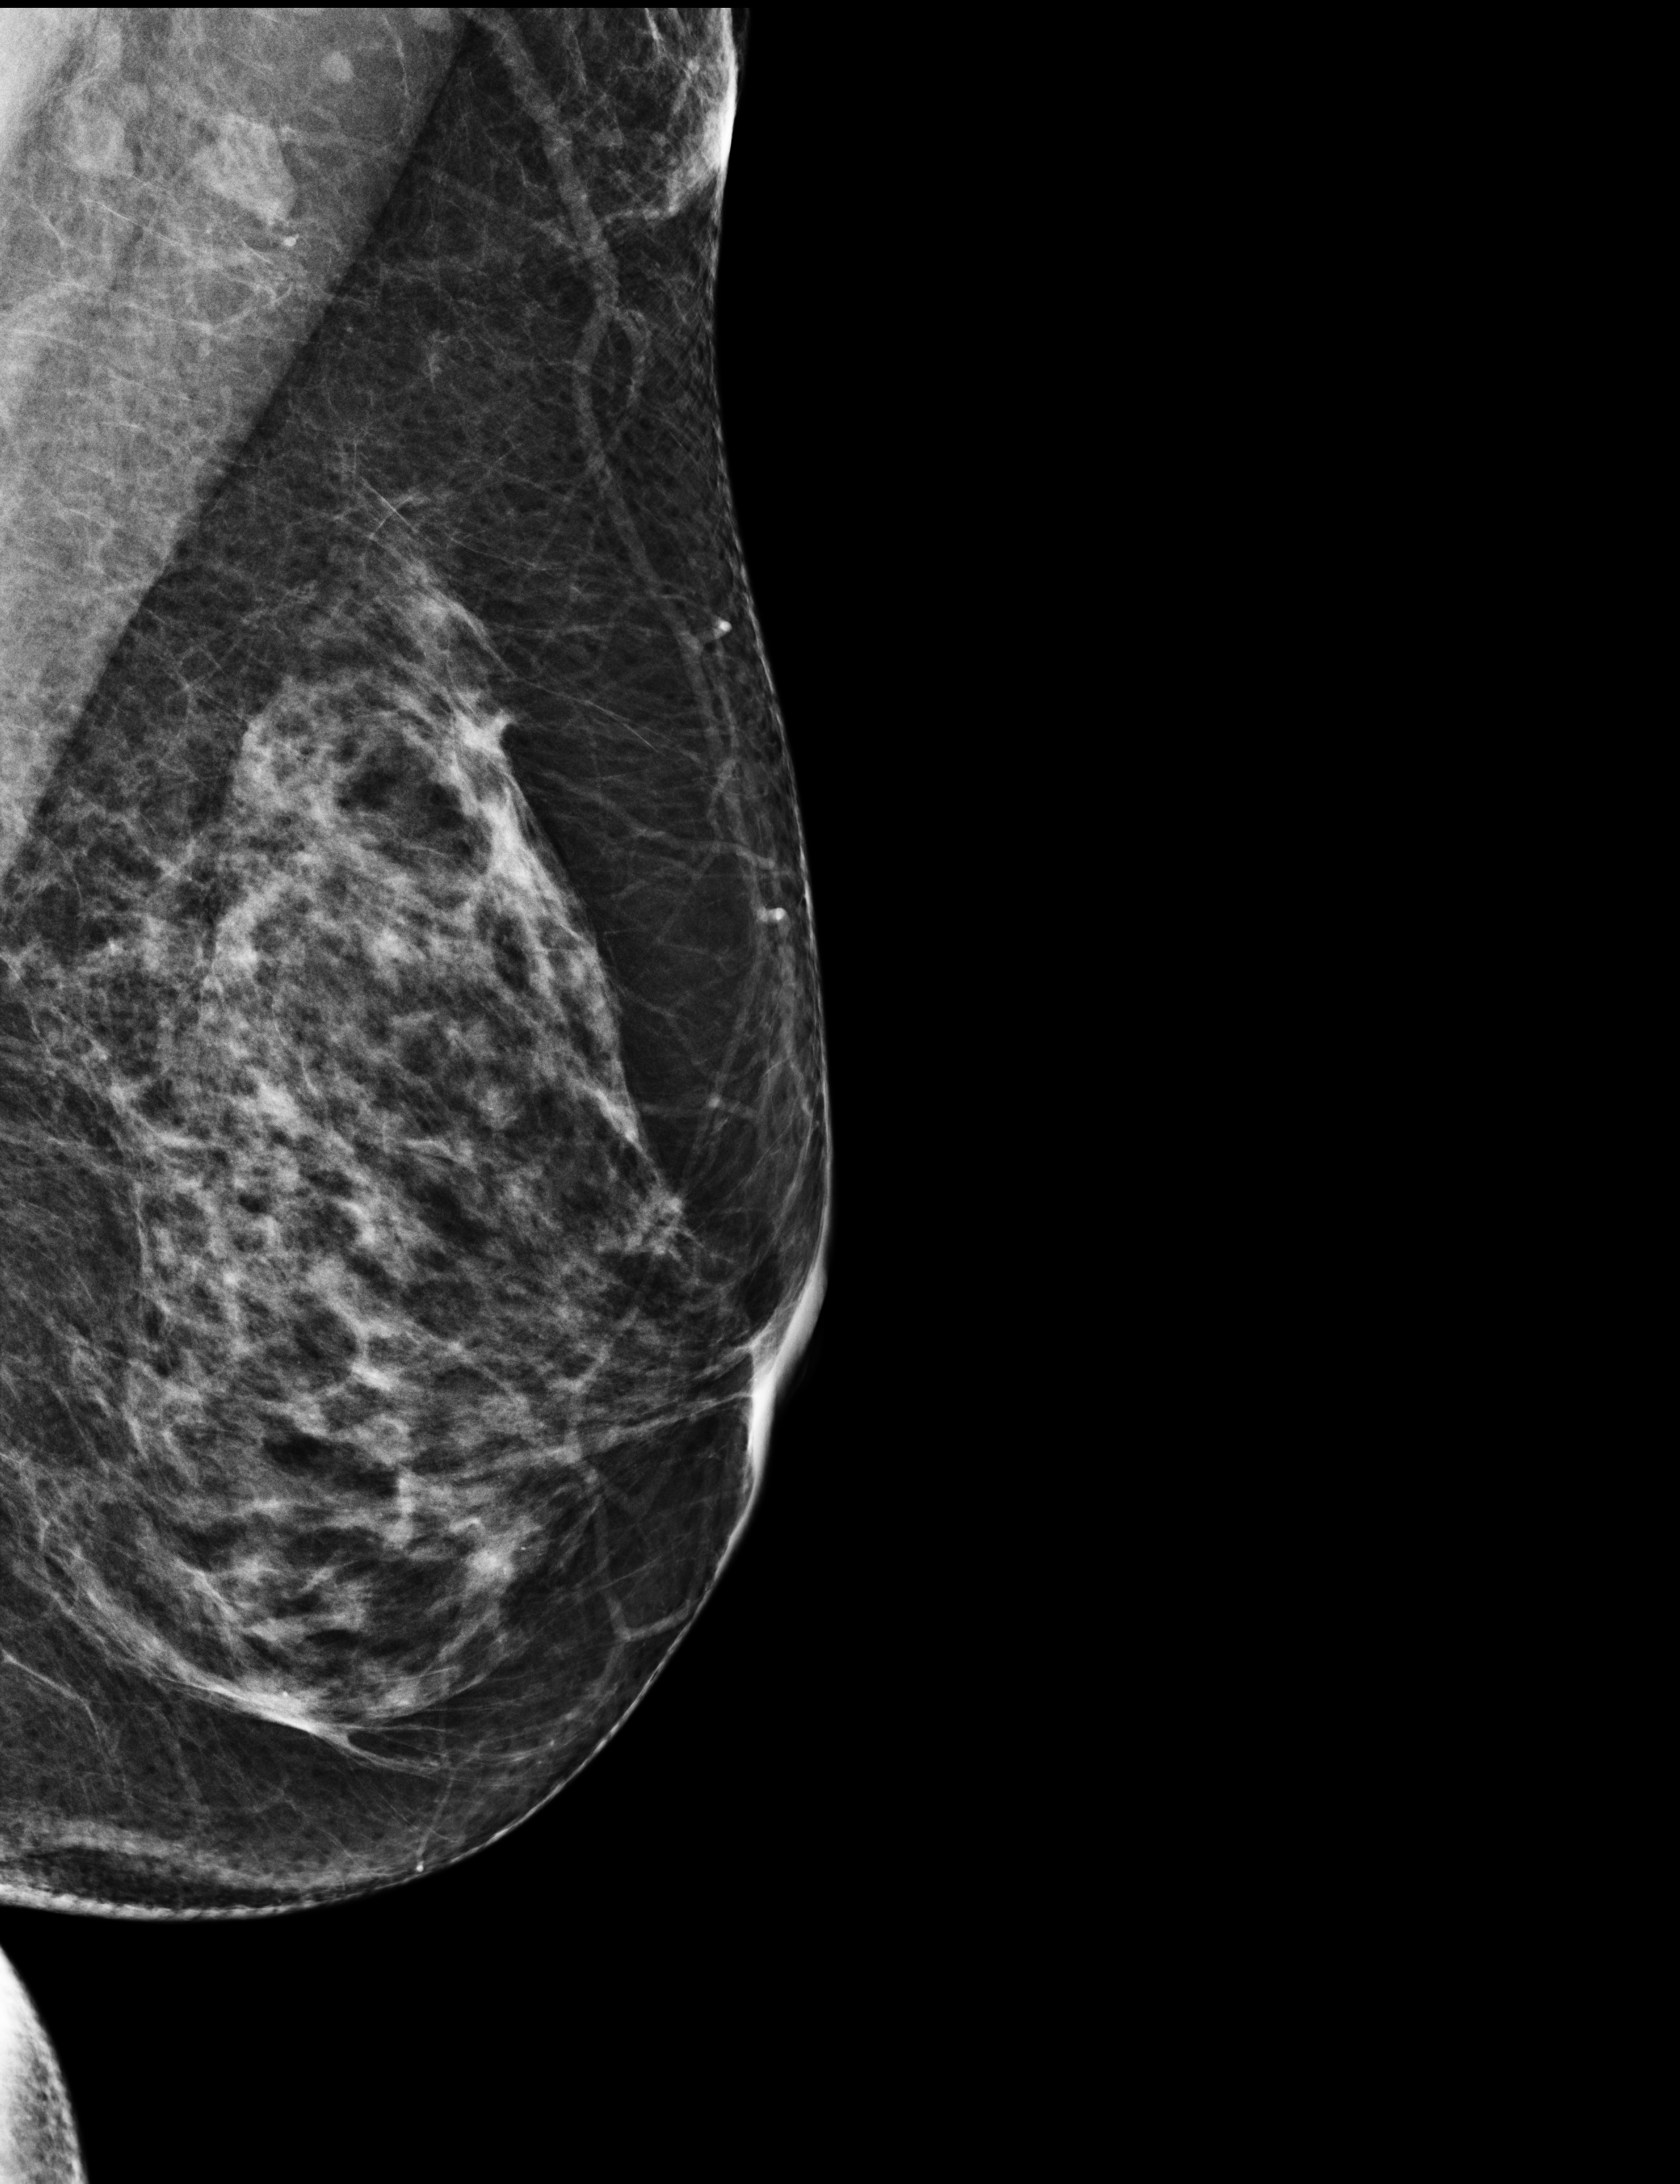
Screening examination, compressed breast thickness 67 mm. Patient: female, 70 years.
Image type: full-field digital mammogram. Breast: left. Projection: mediolateral oblique (MLO) view.